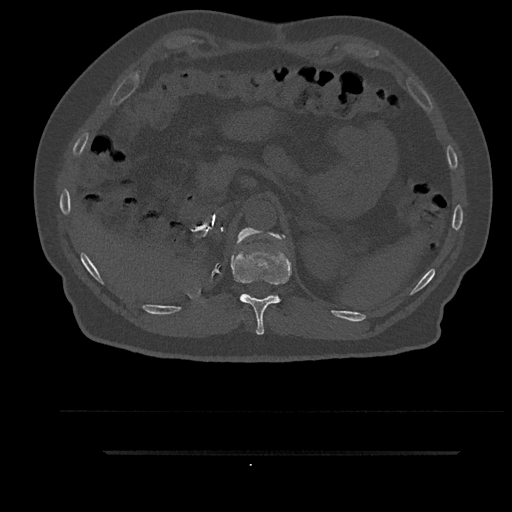
CT including the spine, one axial slice. Position 287 of 797 along the scan axis. Reconstruction kernel Br40s/3. Bone window (W 1800 / L 400 HU). 0.5 mm slice thickness. 512 × 512 image matrix, field of view 432 × 432 mm. Patient: male, 63 years. Case-level facts recorded for this patient, not image findings: primary cancer: renal; vertebrae with lytic lesions (as recorded): T8.
Outlined on this slice (semi-automatically segmented with operator editing):
- T11 vertebra: box from (x=231, y=228) to (x=292, y=335) px
- T12 vertebra: (x=236, y=228)–(x=261, y=245)